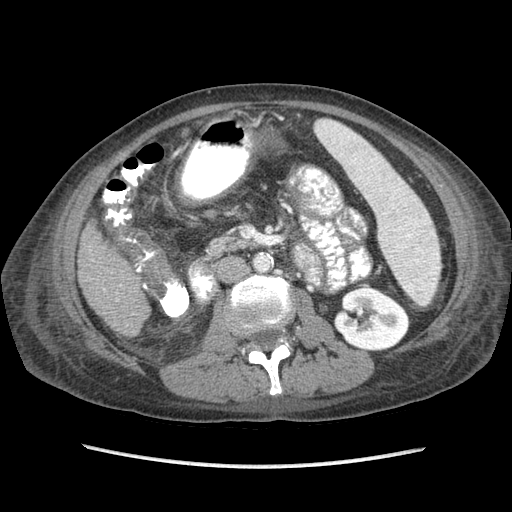
Contrast-enhanced abdominal CT (liver protocol), one axial slice. Position 23 of 87 along the scan axis. Reconstruction kernel STANDARD. Soft-tissue window (W 400 / L 40 HU). 2.5 mm slice thickness. 512 × 512 image matrix, field of view 340 × 340 mm. From the clinical record (not read from this slice): diagnosis: hepatocellular carcinoma (patient treated with transarterial chemoembolisation; whether this scan precedes or follows treatment is not stated here); TNM stage (as recorded): Stage-IIIB; Child-Pugh class: A; tumour nodularity: uninodular.
Outlined on this slice (semi-automatic segmentation, software-assisted and operator-edited):
- liver parenchyma outside the tumour (the mass and vessels are separate outlines, so this box may not span the whole liver): bounding box <78,220,150,335> (left, top, right, bottom; pixels)